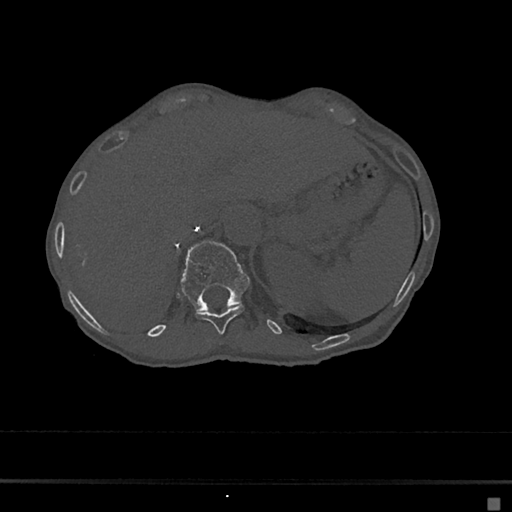
CT including the spine, one axial slice; slice 148 of 797 in the series (ordered by position); 120 kVp; bone window (W 1800 / L 400 HU); 0.5 mm slice thickness; 512 × 512 image matrix, field of view 360 × 360 mm. Female patient, age 68 years. Case-level facts recorded for this patient, not image findings: primary cancer: renal.
Structures marked on this image (semi-automatic segmentation, software-assisted and operator-edited):
- T11 vertebra: box from (x=195, y=304) to (x=245, y=334) px
- T12 vertebra: (x=181, y=241)–(x=250, y=311)